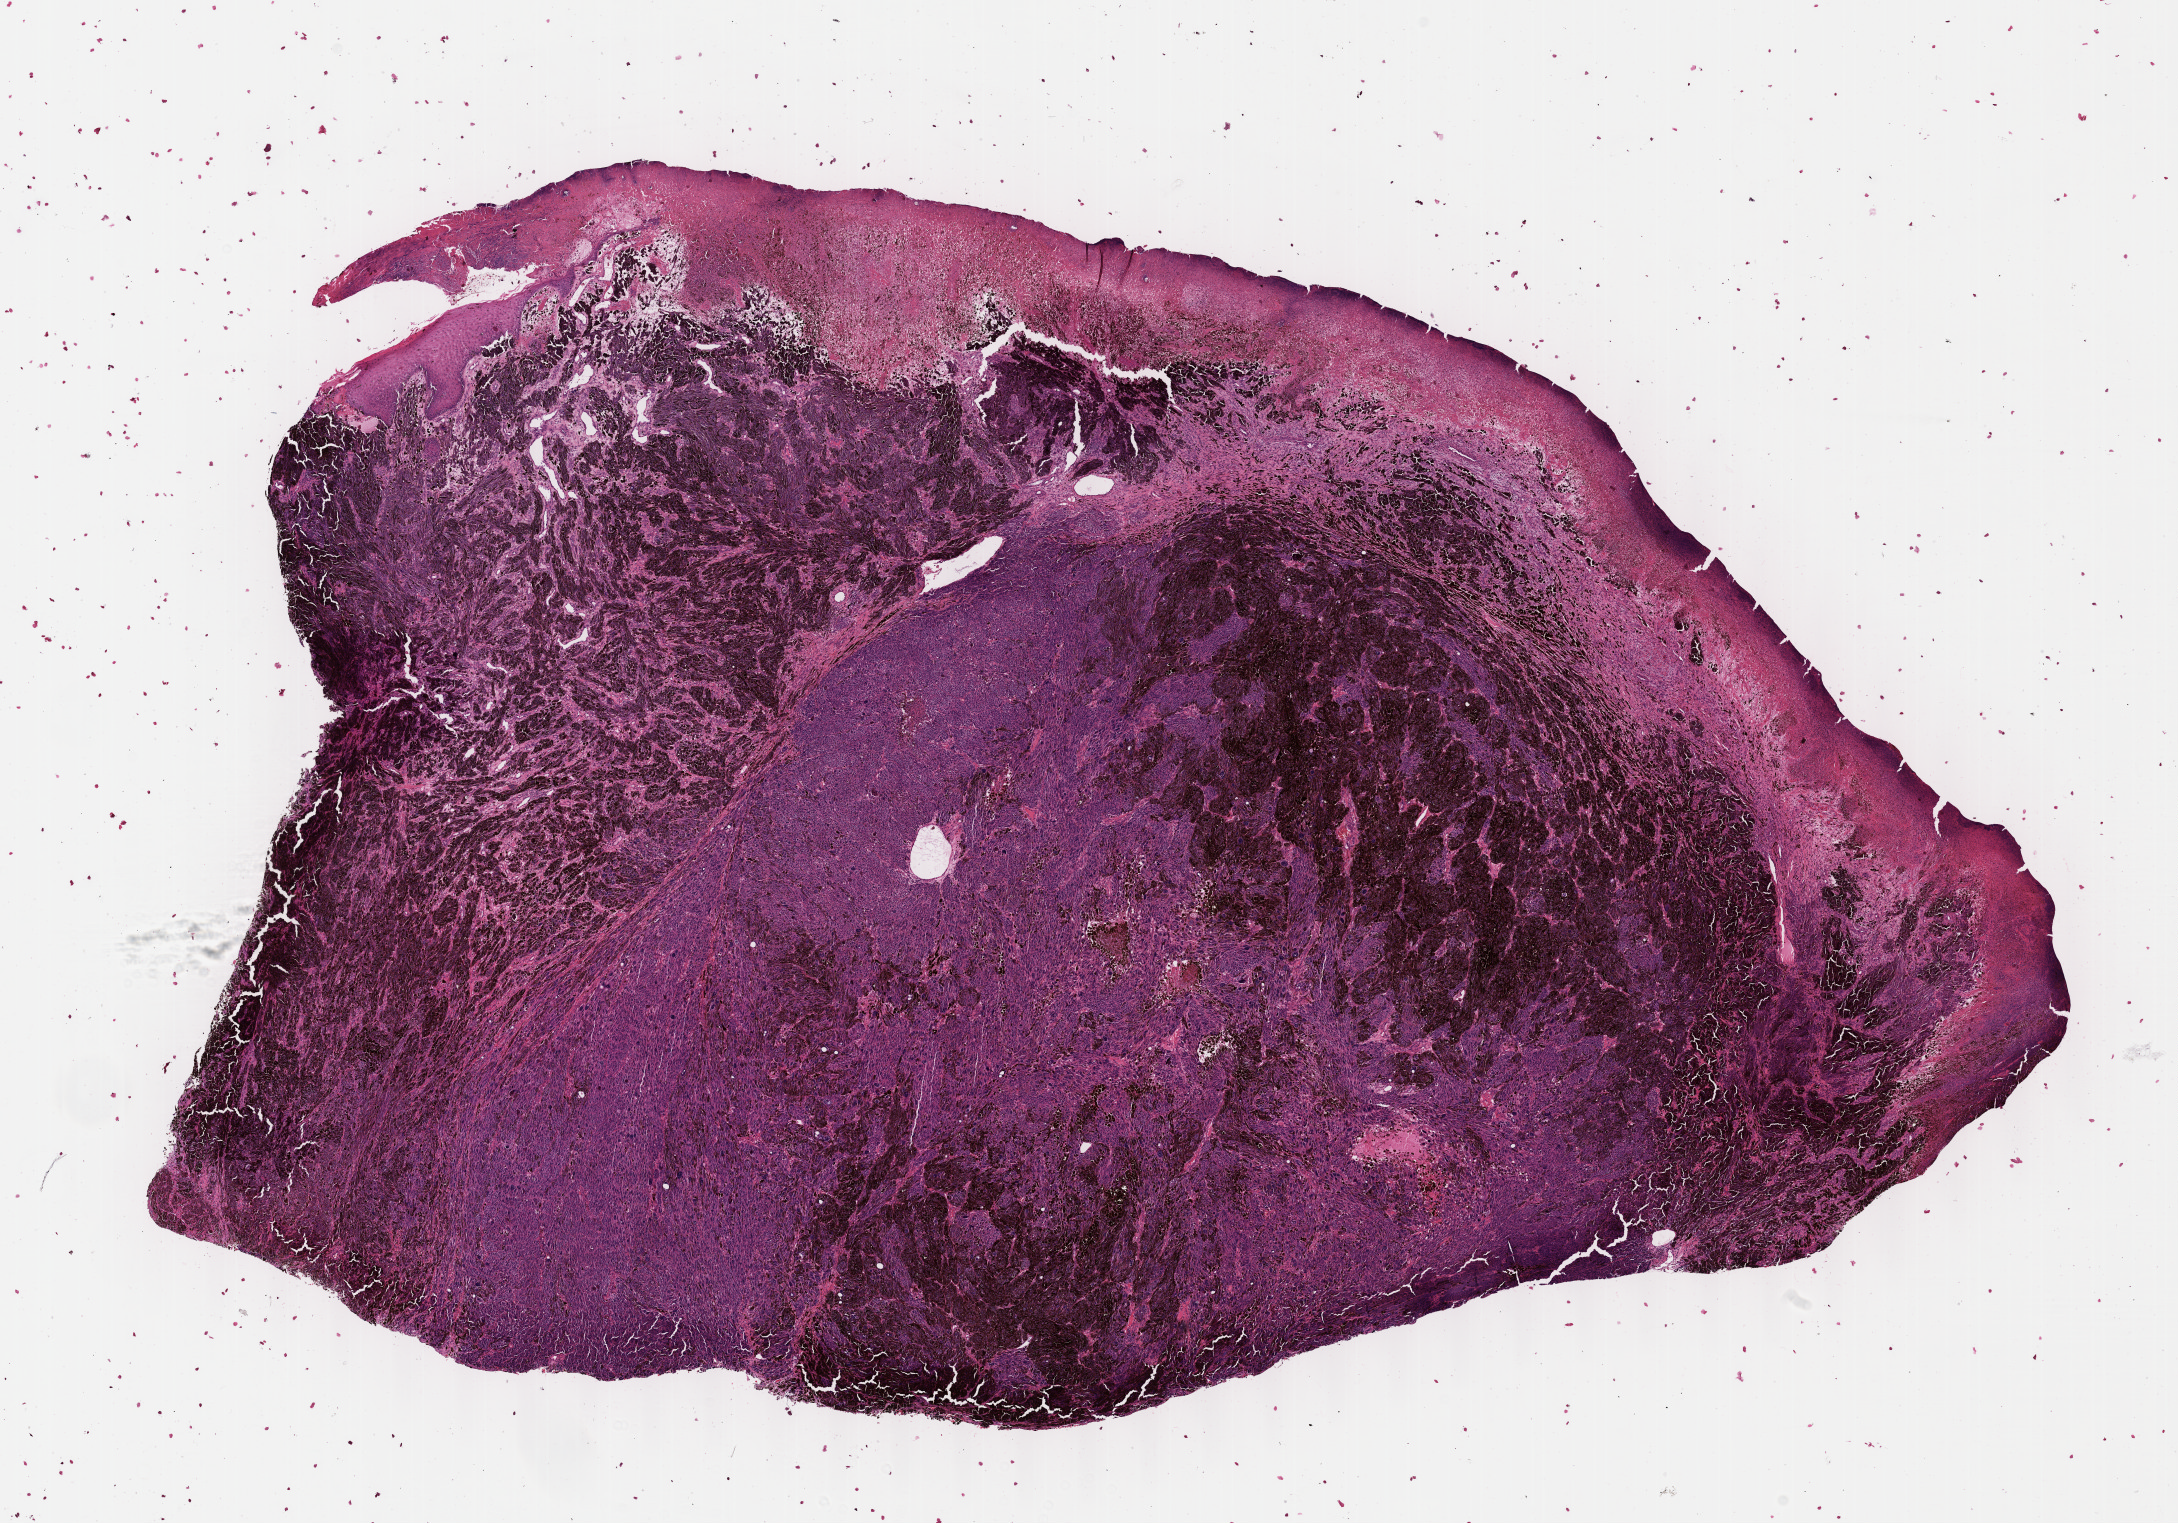
H&E-stained whole-slide image — low-resolution overview of the scanned area, about 17.6 x 12.3 mm (slide scanned at 40x). Formalin-fixed paraffin-embedded (FFPE) diagnostic section. Skin, primary tumour sample. Patient: female, age at initial diagnosis 84 years.
• diagnosis: Malignant melanoma, NOS
• AJCC pathologic stage: IIIB (7th edition)